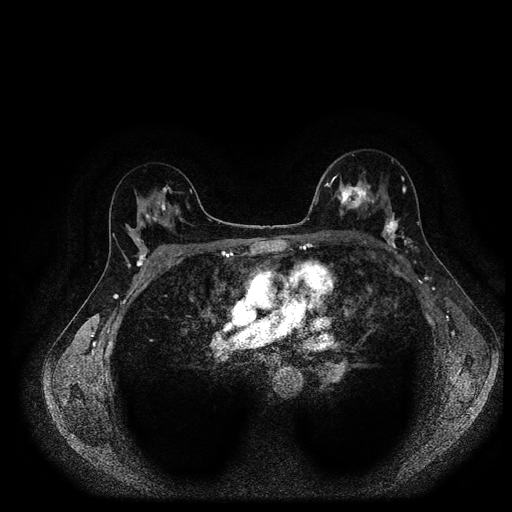
Breast MRI (dynamic contrast-enhanced, multi-phase), one axial slice; slice 64 of 116 in the series (ordered by position); dynamic contrast-enhanced series, time point 2 of 5 at this slice position (early post-contrast); 1.5 T; TE 2.7 ms, TR 5.4 ms; 2 mm slice thickness; 512 × 512 image matrix. Patient: female, 40 years.
Outlined on this slice (semi-automatically segmented with operator editing):
- breast lesion (labelled 'tumour' in the annotation; benign lesions carry a separate 'benign' label): bounding box <332,179,371,215> (left, top, right, bottom; pixels)